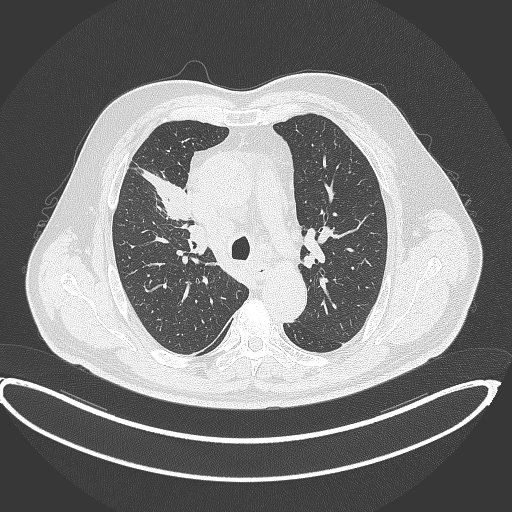
Chest CT, one axial slice. Slice 280 of 390 in the series (ordered by position). 120 kVp. Lung window (W 1500 / L -600 HU). 1 mm slice thickness. 512 × 512 image matrix, field of view 448 × 448 mm. Male patient, age 62 years. Case-level facts recorded for this patient, not image findings: clinical TNM (as recorded): T1c N3 M1c.
Annotated regions visible in this slice (rectangle marked by the reading radiologist):
- lung tumour (recorded histology: adenocarcinoma): bounding box <138,167,195,223> (left, top, right, bottom; pixels)